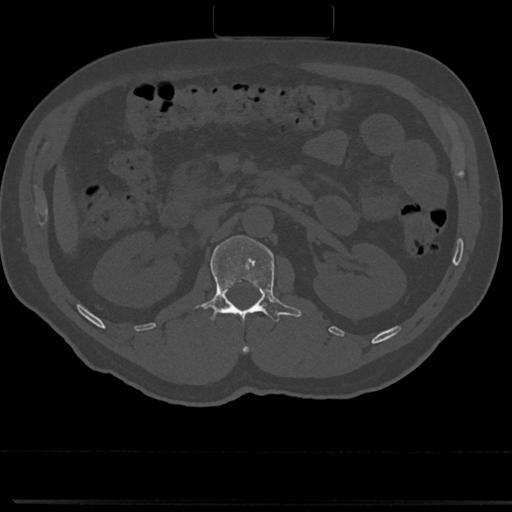
CT including the spine, one axial slice; slice 80 of 817 in the series (ordered by position); bone window (W 1800 / L 400 HU); 0.5 mm slice thickness; 512 × 512 image matrix, field of view 355 × 355 mm. Patient: male, 61 years. From the clinical record (not read from this slice): primary cancer: prostate.
Outlined on this slice (semi-automatically segmented with operator editing):
- L1 vertebra: bounding box (x1, y1, x2, y2) in pixels: (191, 237, 300, 323)